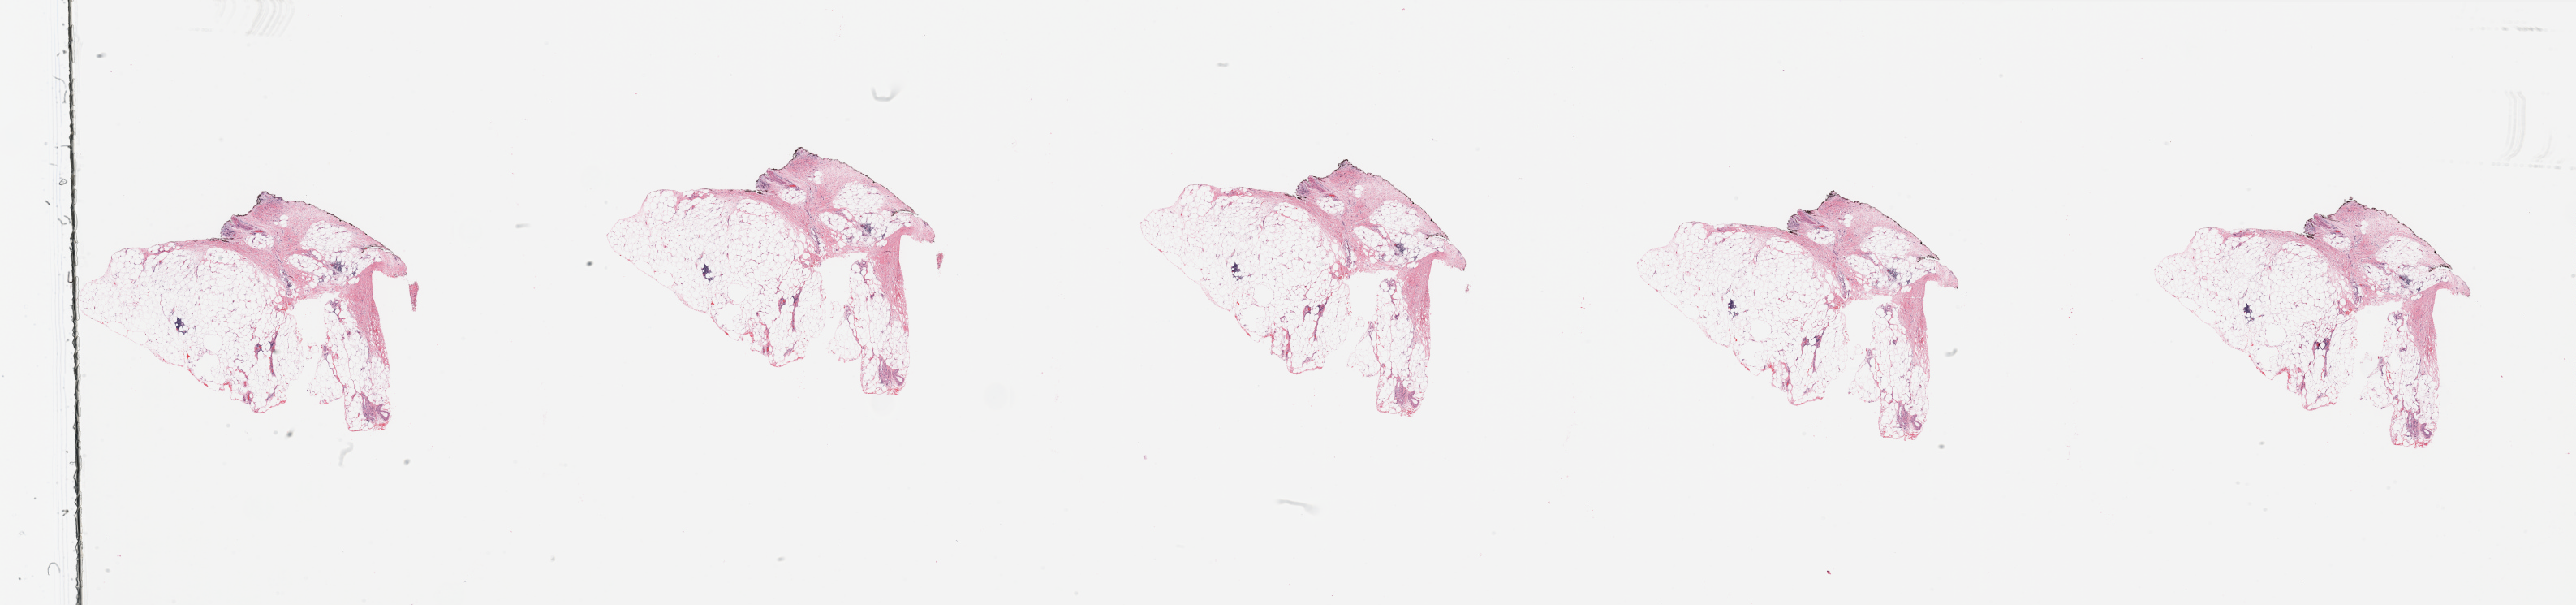
Whole-slide histology image, H&E-stained — low-resolution overview of the scanned area, about 50.2 x 11.8 mm (acquisition: 20x scan), normal (non-tumour) tissue sample, sampled site: pancreas. Male, 62 y/o.
* this section: normal (non-tumour) tissue from the same patient
* patient diagnosis: Infiltrating duct carcinoma, NOS